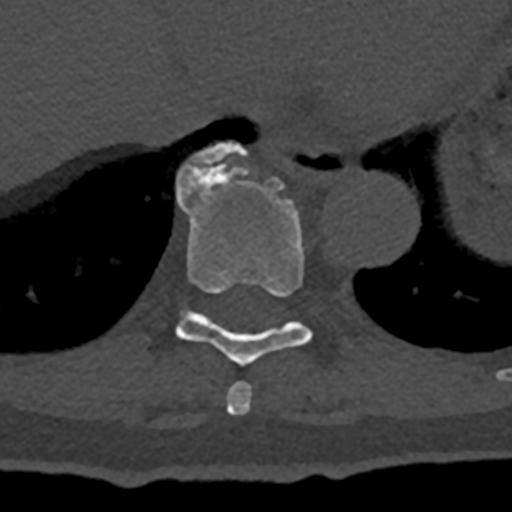
CT including the spine, one axial slice; position 650 of 797 along the scan axis; reconstruction kernel Br40s/3; 120 kVp; bone window (W 1800 / L 400 HU); 0.5 mm slice thickness; 512 × 512 image matrix, field of view 160 × 160 mm. Male patient, age 74 years. From the clinical record (not read from this slice): primary cancer: renal.
Structures marked on this image (semi-automatic segmentation, software-assisted and operator-edited):
- T10 vertebra: bounding box (x1, y1, x2, y2) in pixels: (176, 143, 248, 200)
- T8 vertebra: (226, 381, 252, 415)
- T9 vertebra: (175, 166, 312, 366)